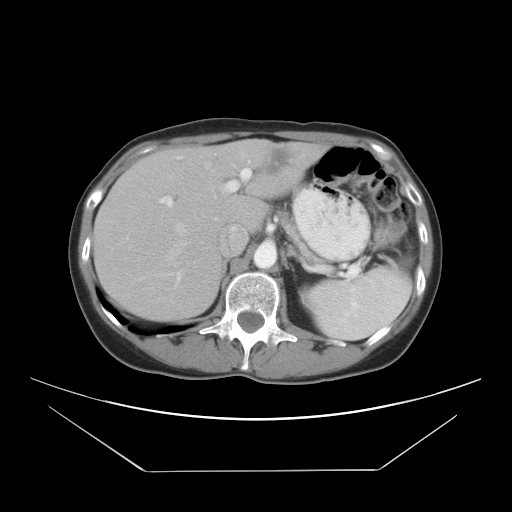
Contrast-enhanced abdominal CT, one axial slice. Slice 19 of 30 in the series (ordered by position). Intravenous contrast given. Soft-tissue window (W 400 / L 40 HU). 7.5 mm slice thickness. 512 × 512 image matrix, field of view 412 × 412 mm. Female patient, age 54 years. Case-level facts recorded for this patient, not image findings: diagnosis: colorectal cancer liver metastases, imaged before liver resection; multiple liver metastases: yes; largest metastasis: 2.5 cm; disease in both lobes: yes.
Structures marked on this image (outlined manually by an expert reader):
- hepatic veins: bounding box <135,163,210,300> (left, top, right, bottom; pixels)
- liver: <96,140,322,319>
- planned liver remnant (the part of the liver to remain after resection): <96,145,265,319>
- portal vein (with intrahepatic branches): <158,155,251,208>
- liver metastasis: <255,148,296,180>